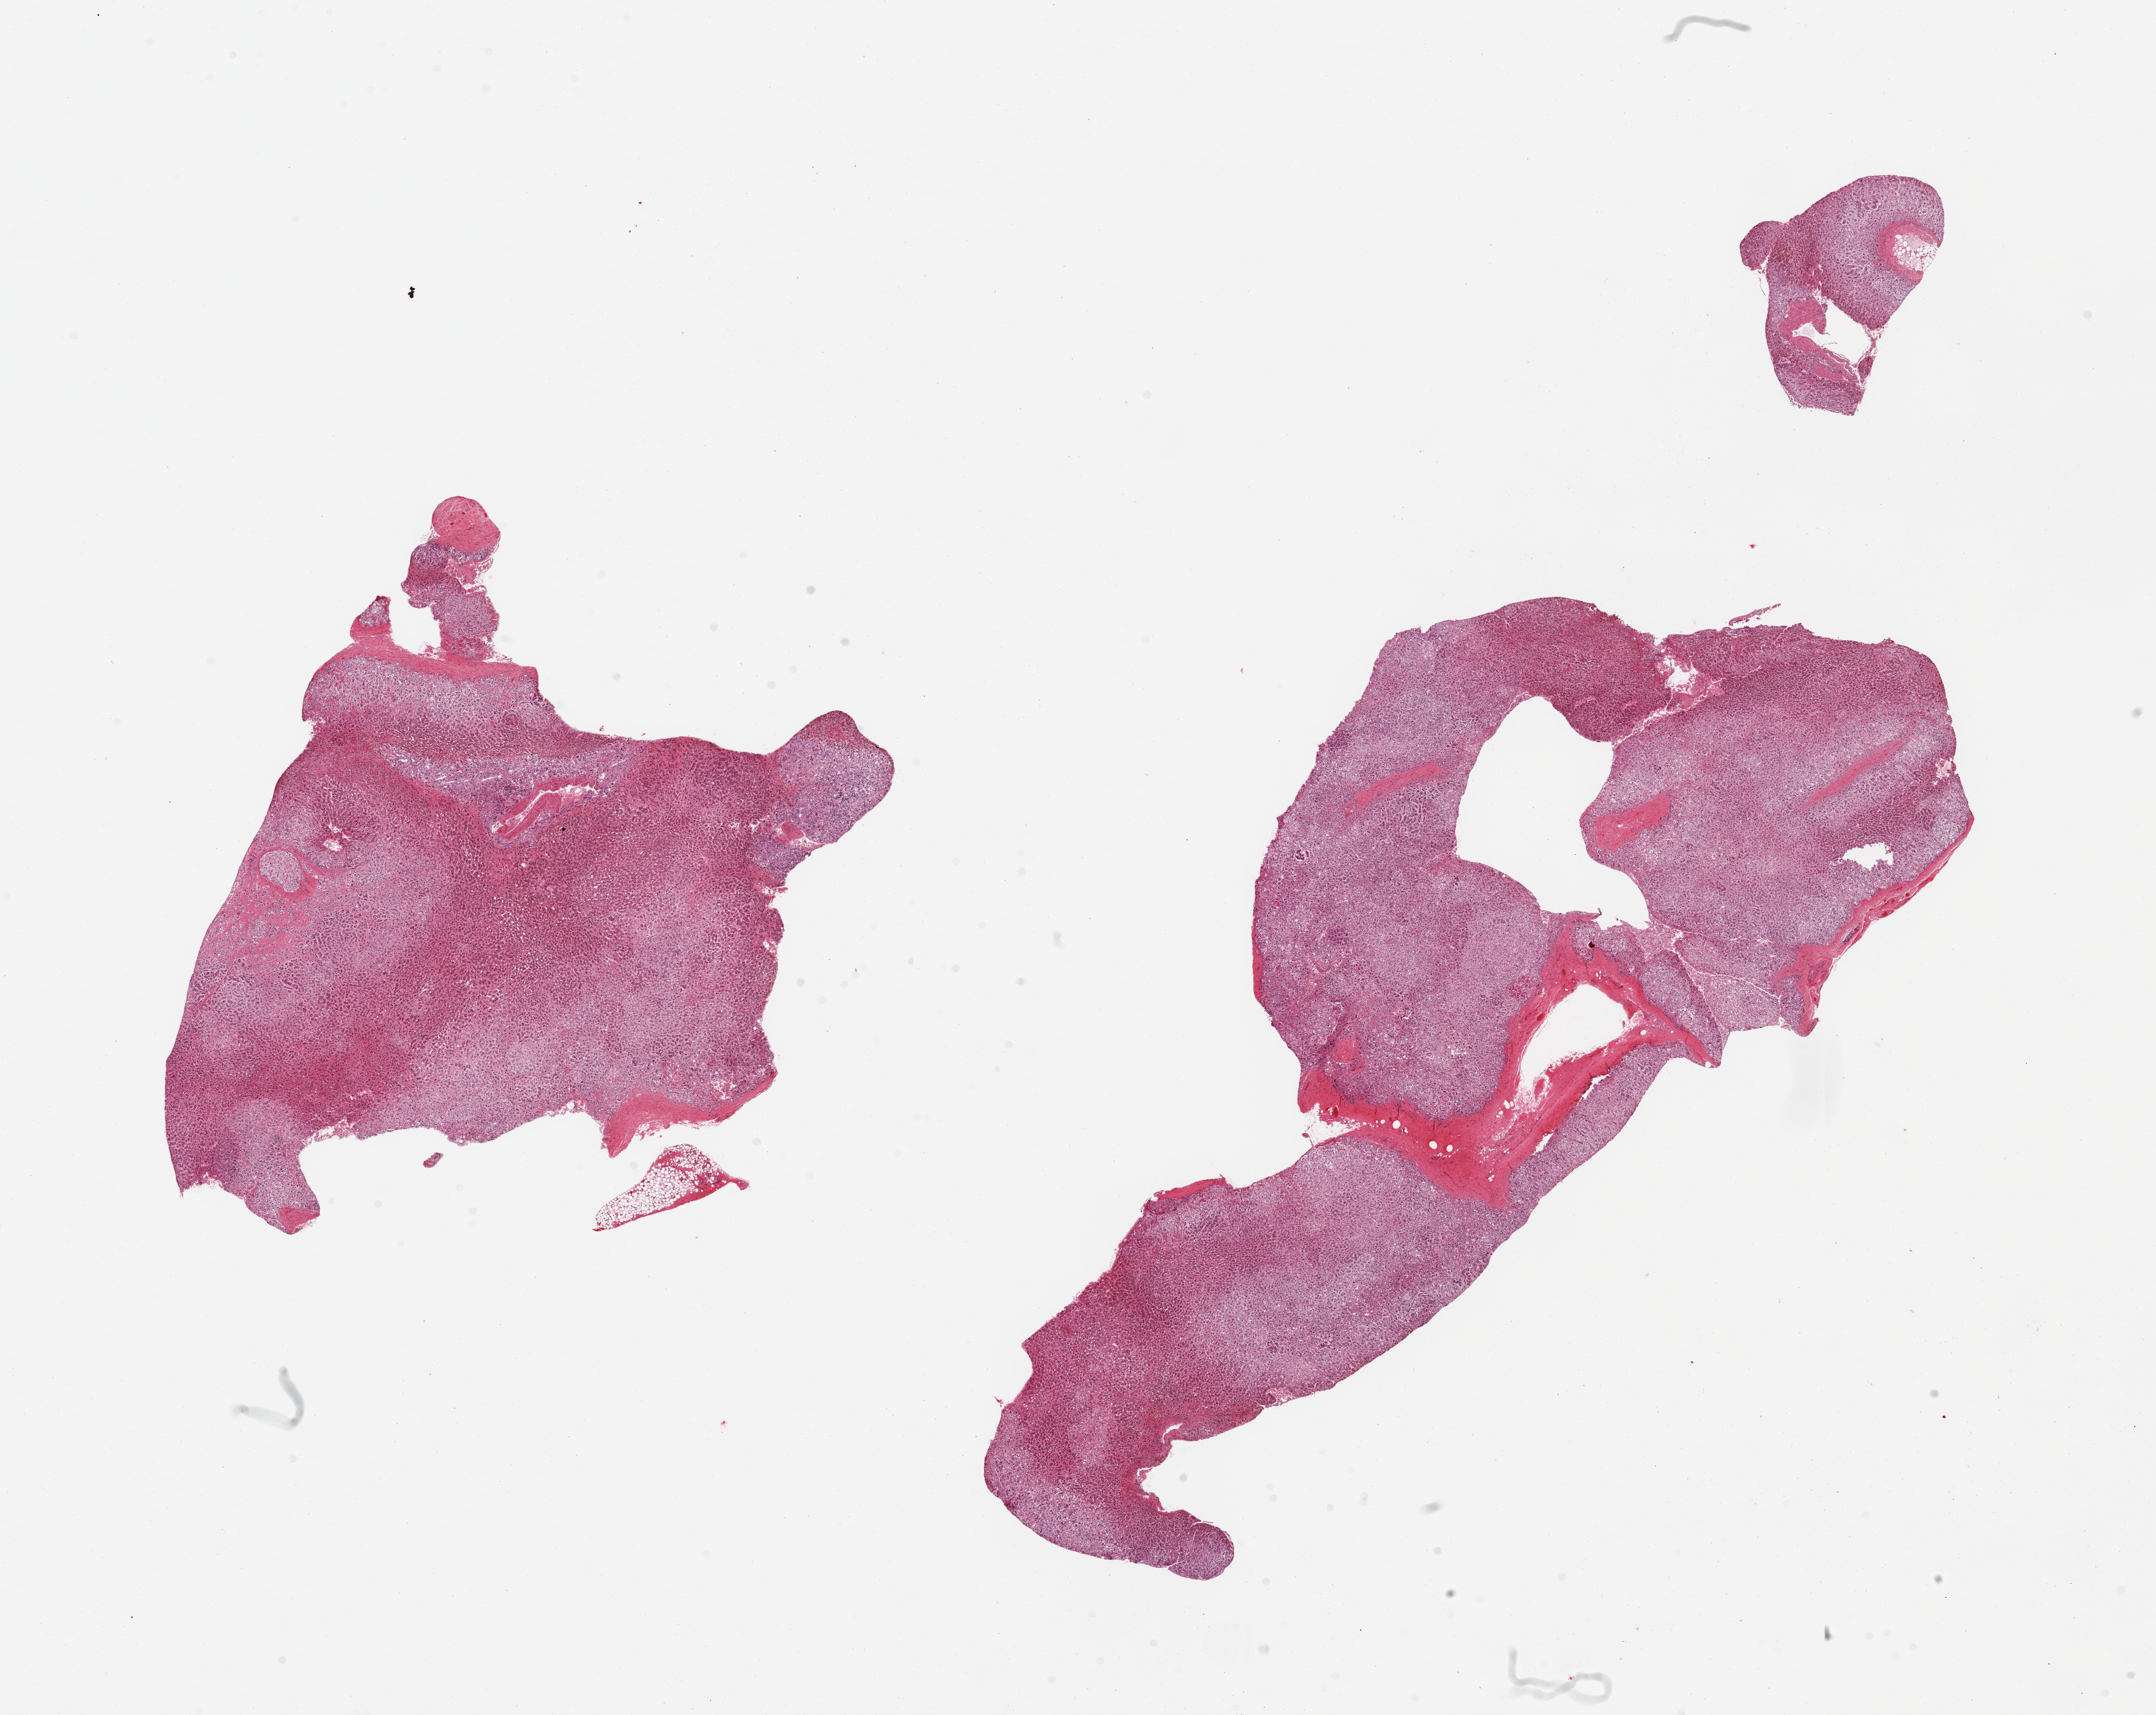
Whole-slide image, H&E stain — whole scanned area (about 25.6 x 20.4 mm, from a 20x scan) shown as a low-resolution overview; PAXgene-fixed paraffin-embedded (PFPE) section; sampled site (target tissue): adrenal gland; tissue donor sample. Male donor.
* reviewer comment on this tissue sample: 2 pieces, all cortex, advanced autolysis